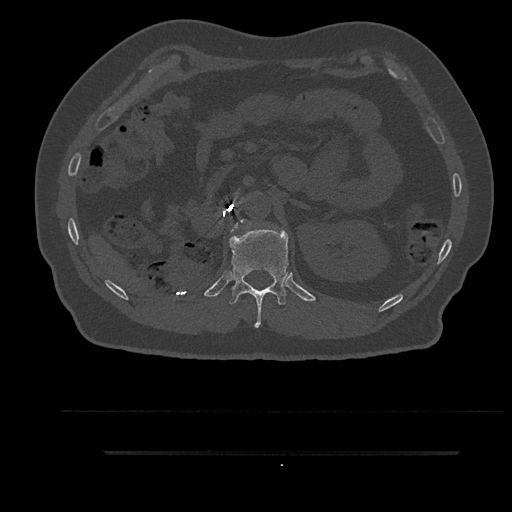
CT including the spine, one axial slice. Slice 235 of 797 in the series (ordered by position). Bone window (W 1800 / L 400 HU). 0.5 mm slice thickness. 512 × 512 image matrix. Patient: male, 63 years. Case-level facts recorded for this patient, not image findings: primary cancer: renal.
Outlined on this slice (semi-automatic segmentation, software-assisted and operator-edited):
- L1 vertebra: bounding box [x1, y1, x2, y2] px = [232, 221, 244, 231]
- T12 vertebra: [229, 229, 289, 328]